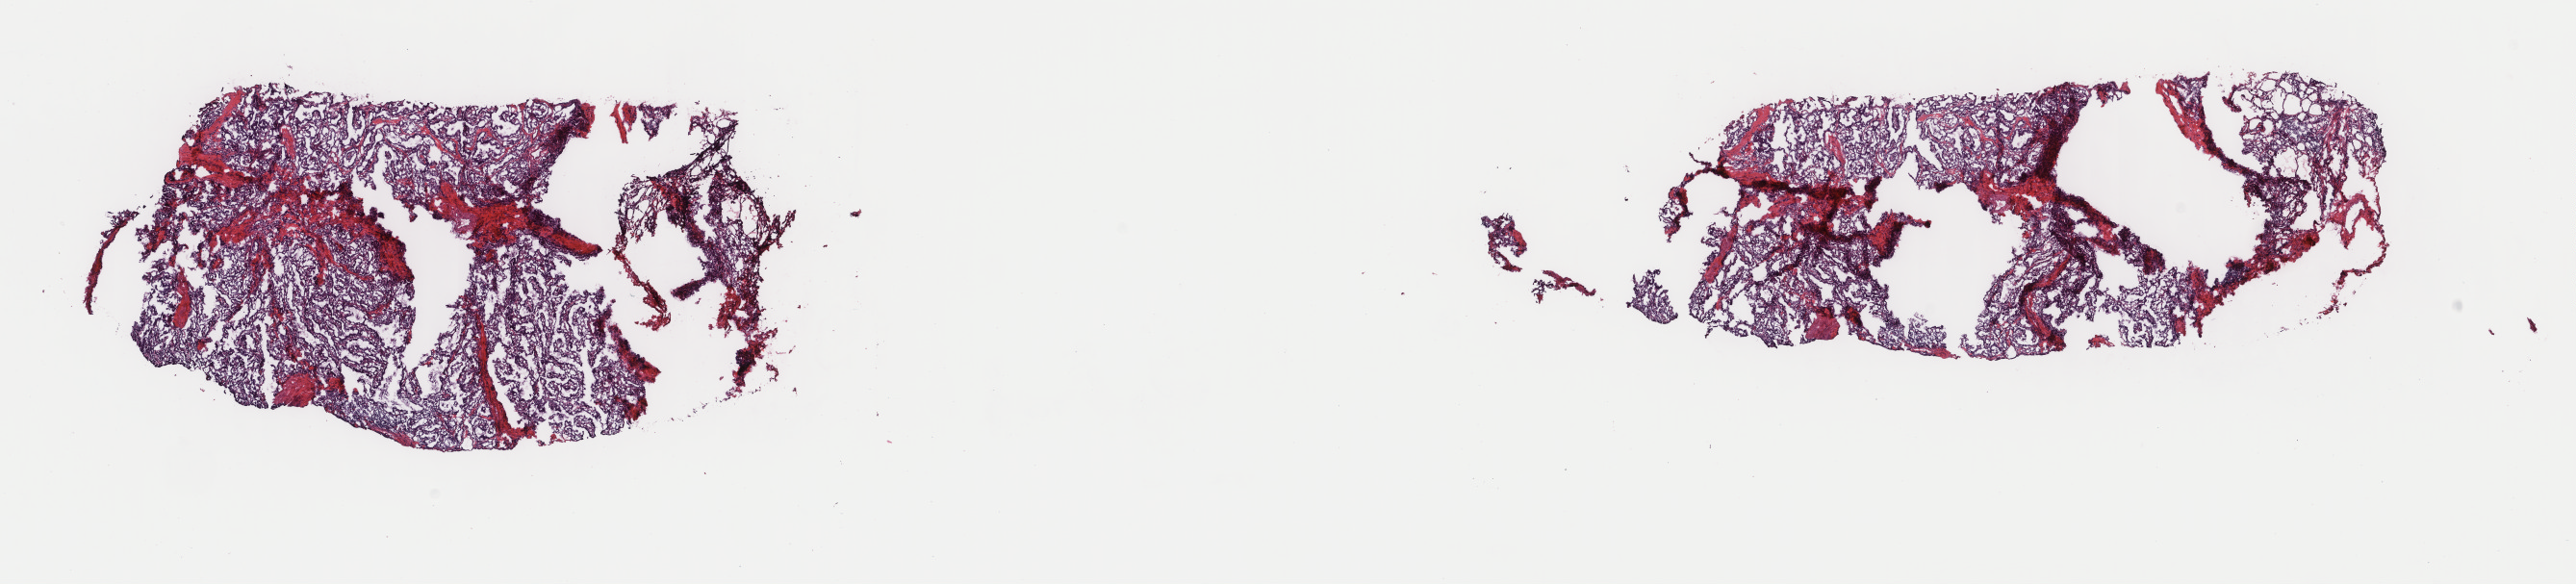
H&E whole-slide image, a low-resolution overview of the entire scanned area, about 21.2 x 4.8 mm; frozen section from the top of the tissue portion; primary tumour sample from the thyroid. Male patient; age at initial diagnosis 72 years. Slide review estimates, as recorded: tumour cells 80%, tumour nuclei 80%, normal cells 0%, stromal cells 20%, necrosis 0%. Infiltration values recorded for this section: lymphocyte infiltration 2%, monocyte infiltration 1%, neutrophil infiltration 0%.
- TNM: T1b N0 MX
- laterality: left
- pathologic diagnosis: Papillary adenocarcinoma, NOS (thyroid gland)
- AJCC pathologic stage: I
- lymph nodes positive (case pathology): 0 of 6 examined